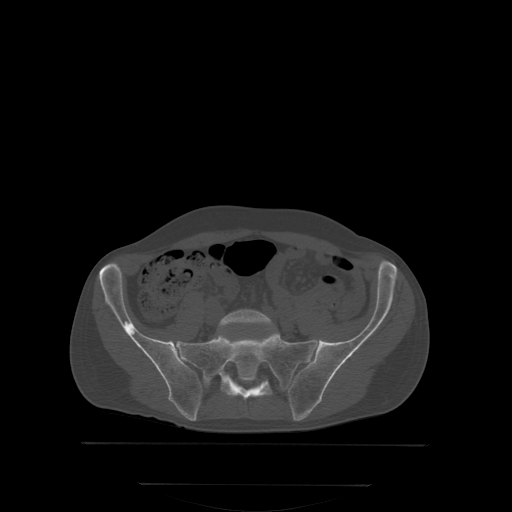
CT including the spine, one axial slice; slice 84 of 350 in the series (ordered by position); bone window (W 1800 / L 400 HU); 512 × 512 image matrix. Patient: male, 58 years. From the clinical record (not read from this slice): primary cancer: prostate; vertebrae with lytic lesions (as recorded): L1.
Outlined on this slice (semi-automatically segmented with operator editing):
- L5 vertebra: box from (x=217, y=309) to (x=273, y=338) px